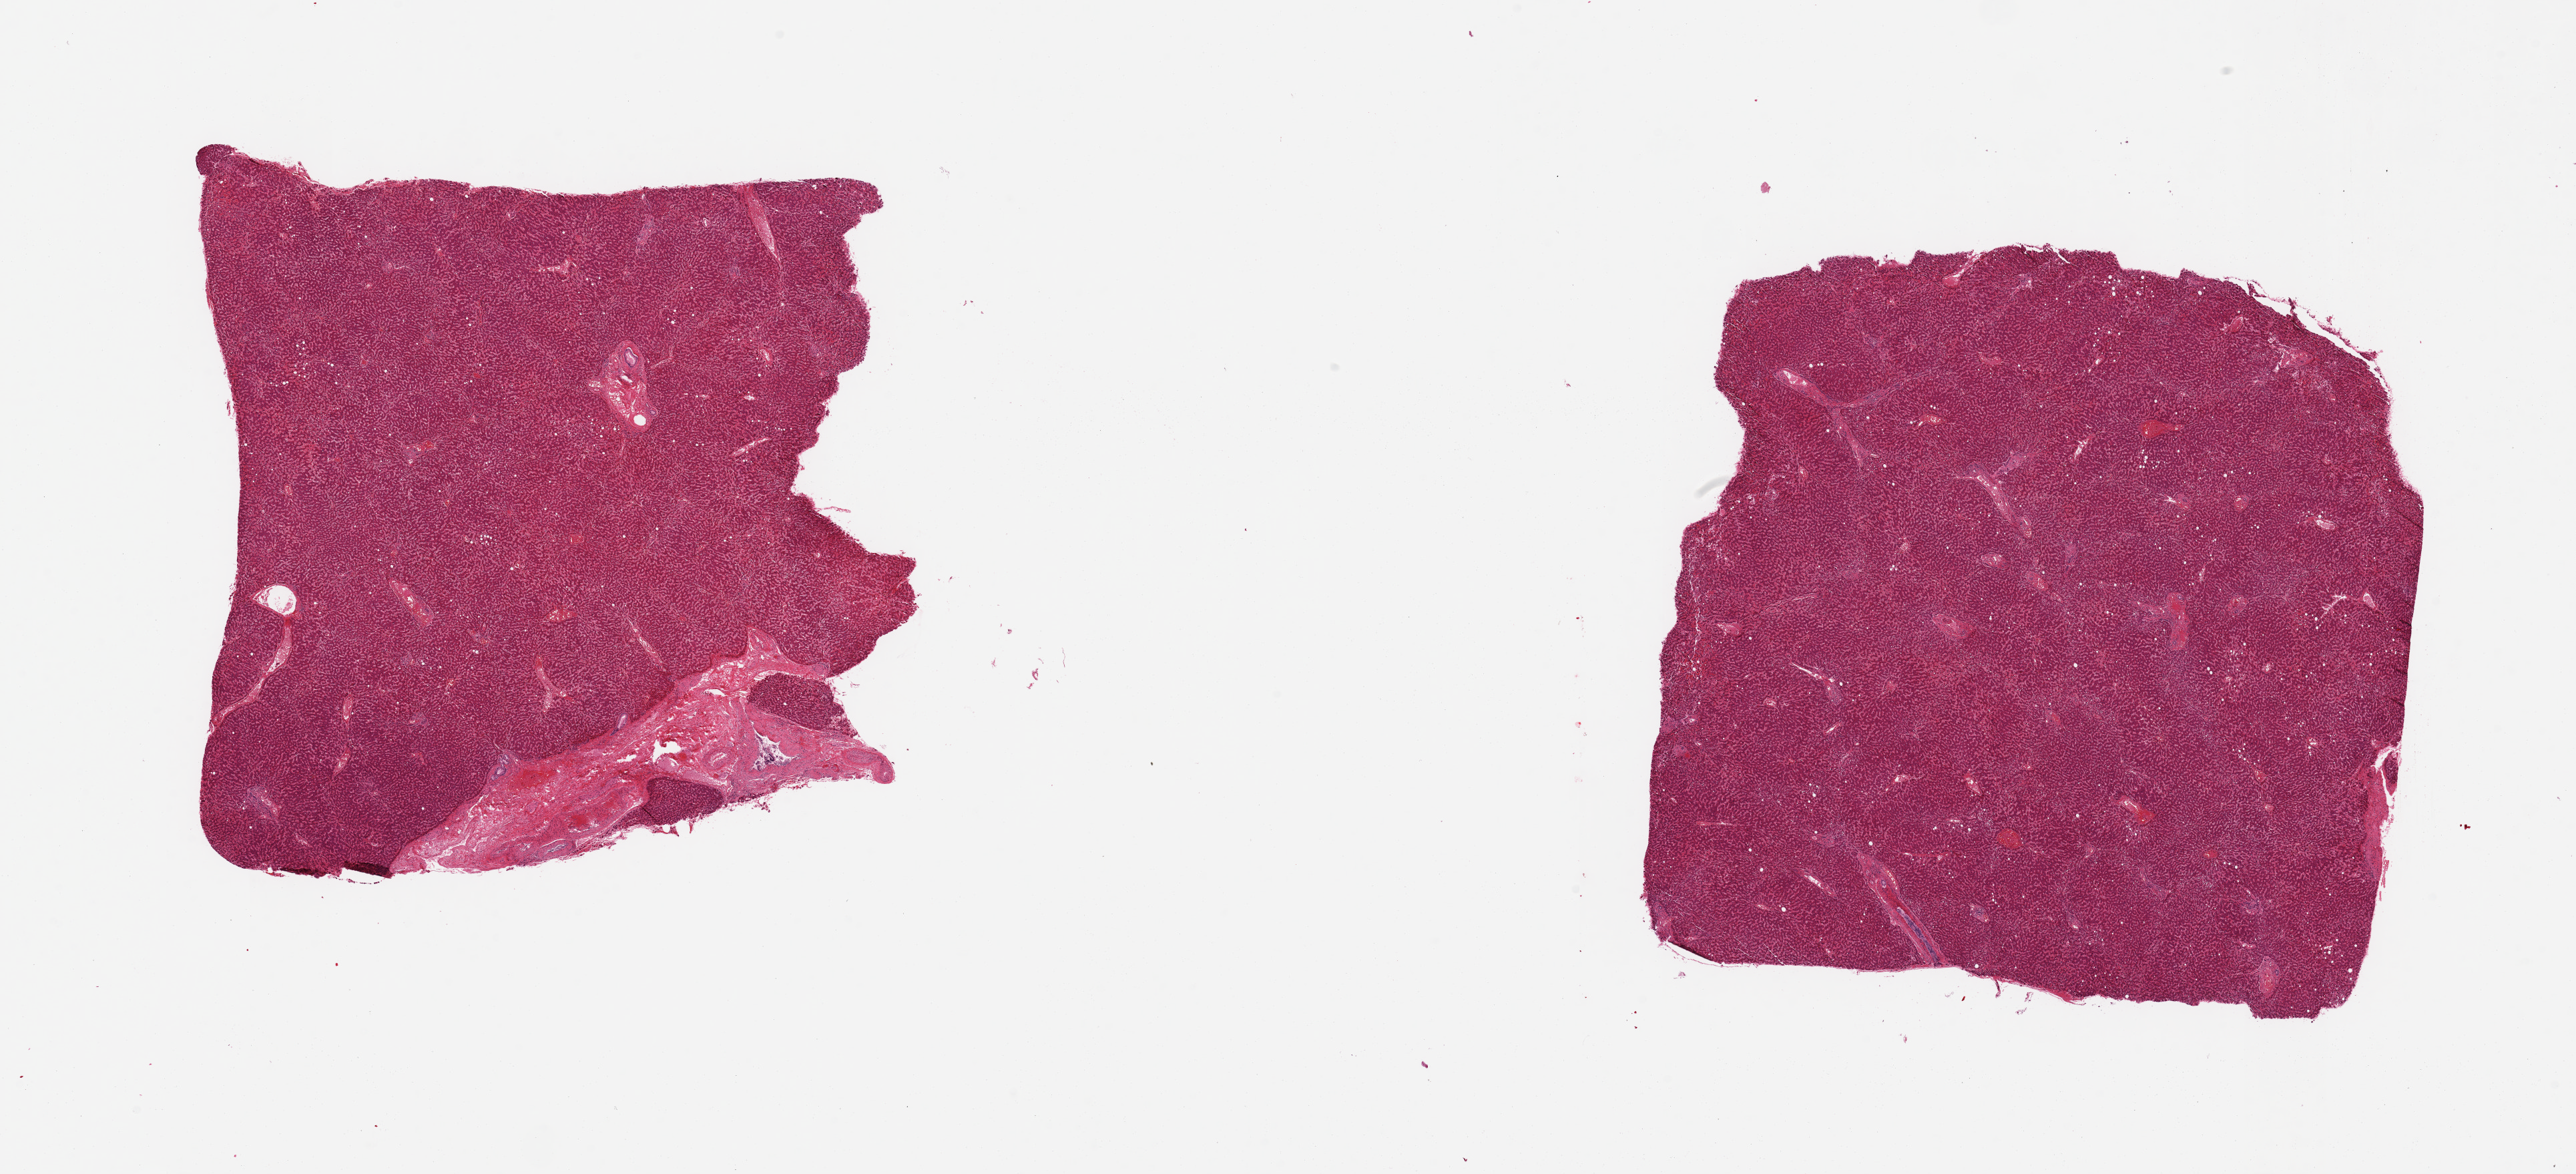
Digitized hematoxylin and eosin (H&E)-stained section — low-resolution overview of the scanned area, about 30.5 x 13.9 mm (acquisition: 20x scan), PAXgene-fixed paraffin-embedded (PFPE) section, target tissue: liver, tissue donor sample. Female donor.
• pathologist's review note for this sample: 2 pieces, mild macrovesicular steatosis ((<10%)